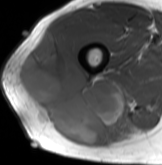
MRI of an extremity soft-tissue mass, one axial slice. Position 54 of 61 along the scan axis. MR volume resampled by the dataset authors to the PET/CT grid (not the native acquisition matrix). 162 × 165 image matrix, field of view 158 × 161 mm. Male patient. From the clinical record (not read from this slice): histological type: poorly differentiated synovial sarcoma; grade: high; site of the primary tumour: right buttock.
Outlined on this slice (expert contour drawn on MRI and transferred to this co-registered scan by the dataset authors):
- gross tumour volume including surrounding oedema: bounding box [x1, y1, x2, y2] px = [16, 31, 136, 146]
- gross tumour volume (mass): [16, 31, 122, 146]